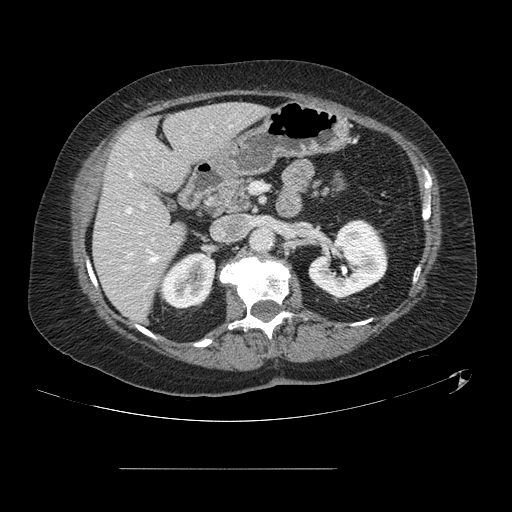
Contrast-enhanced abdominal CT, one axial slice; slice 58 of 148 in the series (ordered by position); intravenous contrast given; soft-tissue window (W 400 / L 40 HU); 2.5 mm slice thickness; 512 × 512 image matrix. Female patient, age 75 years. From the clinical record (not read from this slice): diagnosis: colorectal cancer liver metastases, imaged before liver resection; multiple liver metastases: no; largest metastasis: 2.4 cm; chemotherapy before resection: no.
Outlined on this slice (outlined manually by an expert reader):
- hepatic veins: bounding box [x1, y1, x2, y2] px = [127, 174, 158, 262]
- liver: [94, 105, 265, 321]
- planned liver remnant (the part of the liver to remain after resection): [94, 105, 265, 321]
- portal vein (with intrahepatic branches): [129, 205, 144, 255]